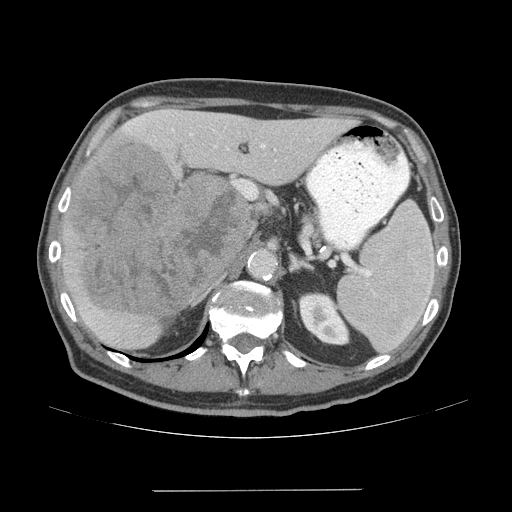
Contrast-enhanced abdominal CT (liver protocol), one axial slice; position 36 of 77 along the scan axis; 140 kVp; soft-tissue window (W 400 / L 40 HU); 512 × 512 image matrix, field of view 400 × 400 mm. From the clinical record (not read from this slice): diagnosis: hepatocellular carcinoma (patient treated with transarterial chemoembolisation; whether this scan precedes or follows treatment is not stated here); TNM stage (as recorded): Stage-IVA; Child-Pugh class: A; tumour differentiation: well differentiated; tumour nodularity: uninodular.
Structures marked on this image (semi-automatically segmented with operator editing):
- liver parenchyma outside the tumour (the mass and vessels are separate outlines, so this box may not span the whole liver): bounding box <62,108,356,348> (left, top, right, bottom; pixels)
- mass: <65,139,253,317>
- liver vessels: <125,115,265,184>